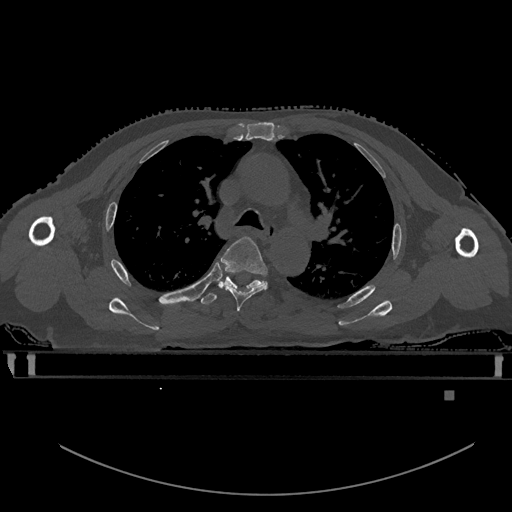
CT including the spine, one axial slice; slice 389 of 969 in the series (ordered by position); bone window (W 1800 / L 400 HU); 0.5 mm slice thickness; 512 × 512 image matrix, field of view 456 × 456 mm. Patient: male, 82 years. Case-level facts recorded for this patient, not image findings: primary cancer: prostate.
Outlined on this slice (semi-automatically segmented with operator editing):
- T4 vertebra: bounding box [x1, y1, x2, y2] px = [220, 236, 268, 313]
- T5 vertebra: [201, 272, 263, 305]